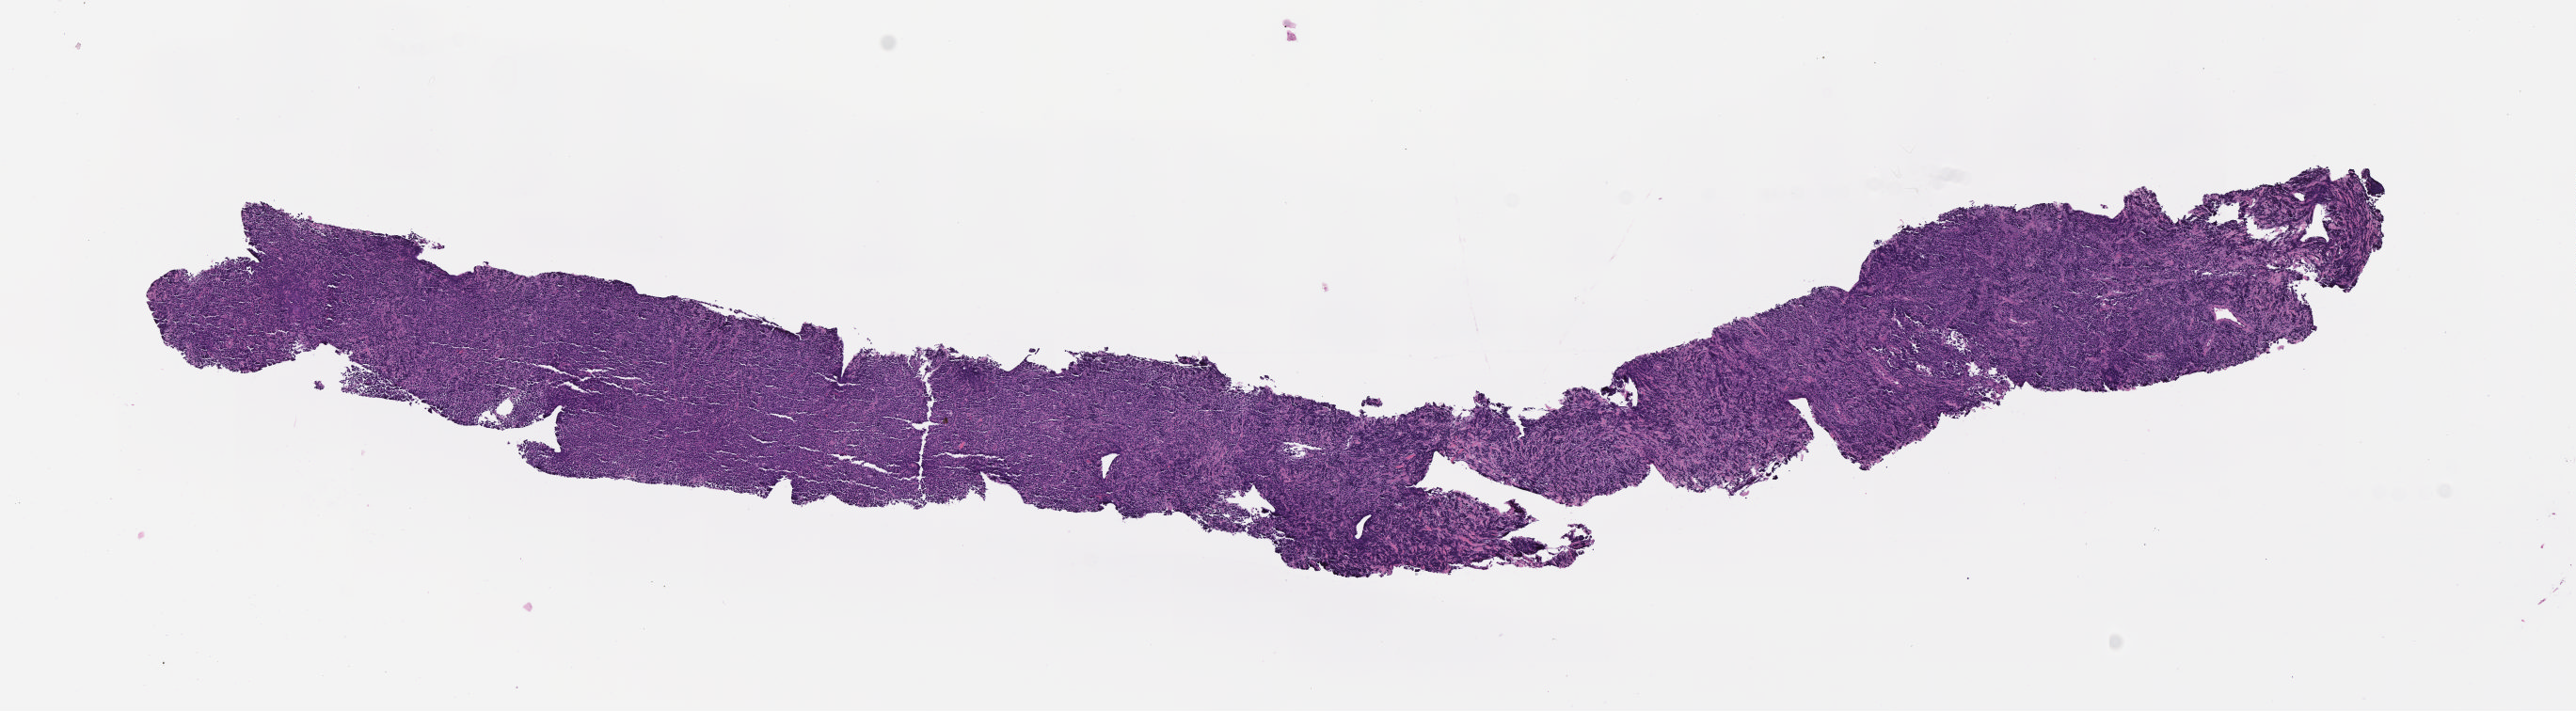
Digitized hematoxylin and eosin (H&E)-stained section — shown as a low-resolution overview of the whole scanned area (about 11.1 x 3.1 mm), specimen: tumor tissue, site: kidney. Male patient; age at initial diagnosis 9 years.
Diagnosis: Burkitt lymphoma, NOS.